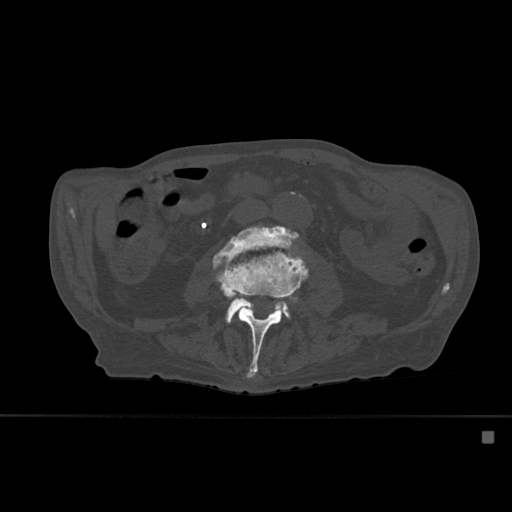
CT including the spine, one axial slice. Position 209 of 527 along the scan axis. Bone window (W 1800 / L 400 HU). 1.5 mm slice thickness. 512 × 512 image matrix, field of view 373 × 373 mm. Male patient, age 78 years. From the clinical record (not read from this slice): primary cancer: prostate.
Structures marked on this image (semi-automatically segmented with operator editing):
- L3 vertebra: box from (x=213, y=232) to (x=309, y=378) px
- L4 vertebra: (x=213, y=227)–(x=298, y=323)